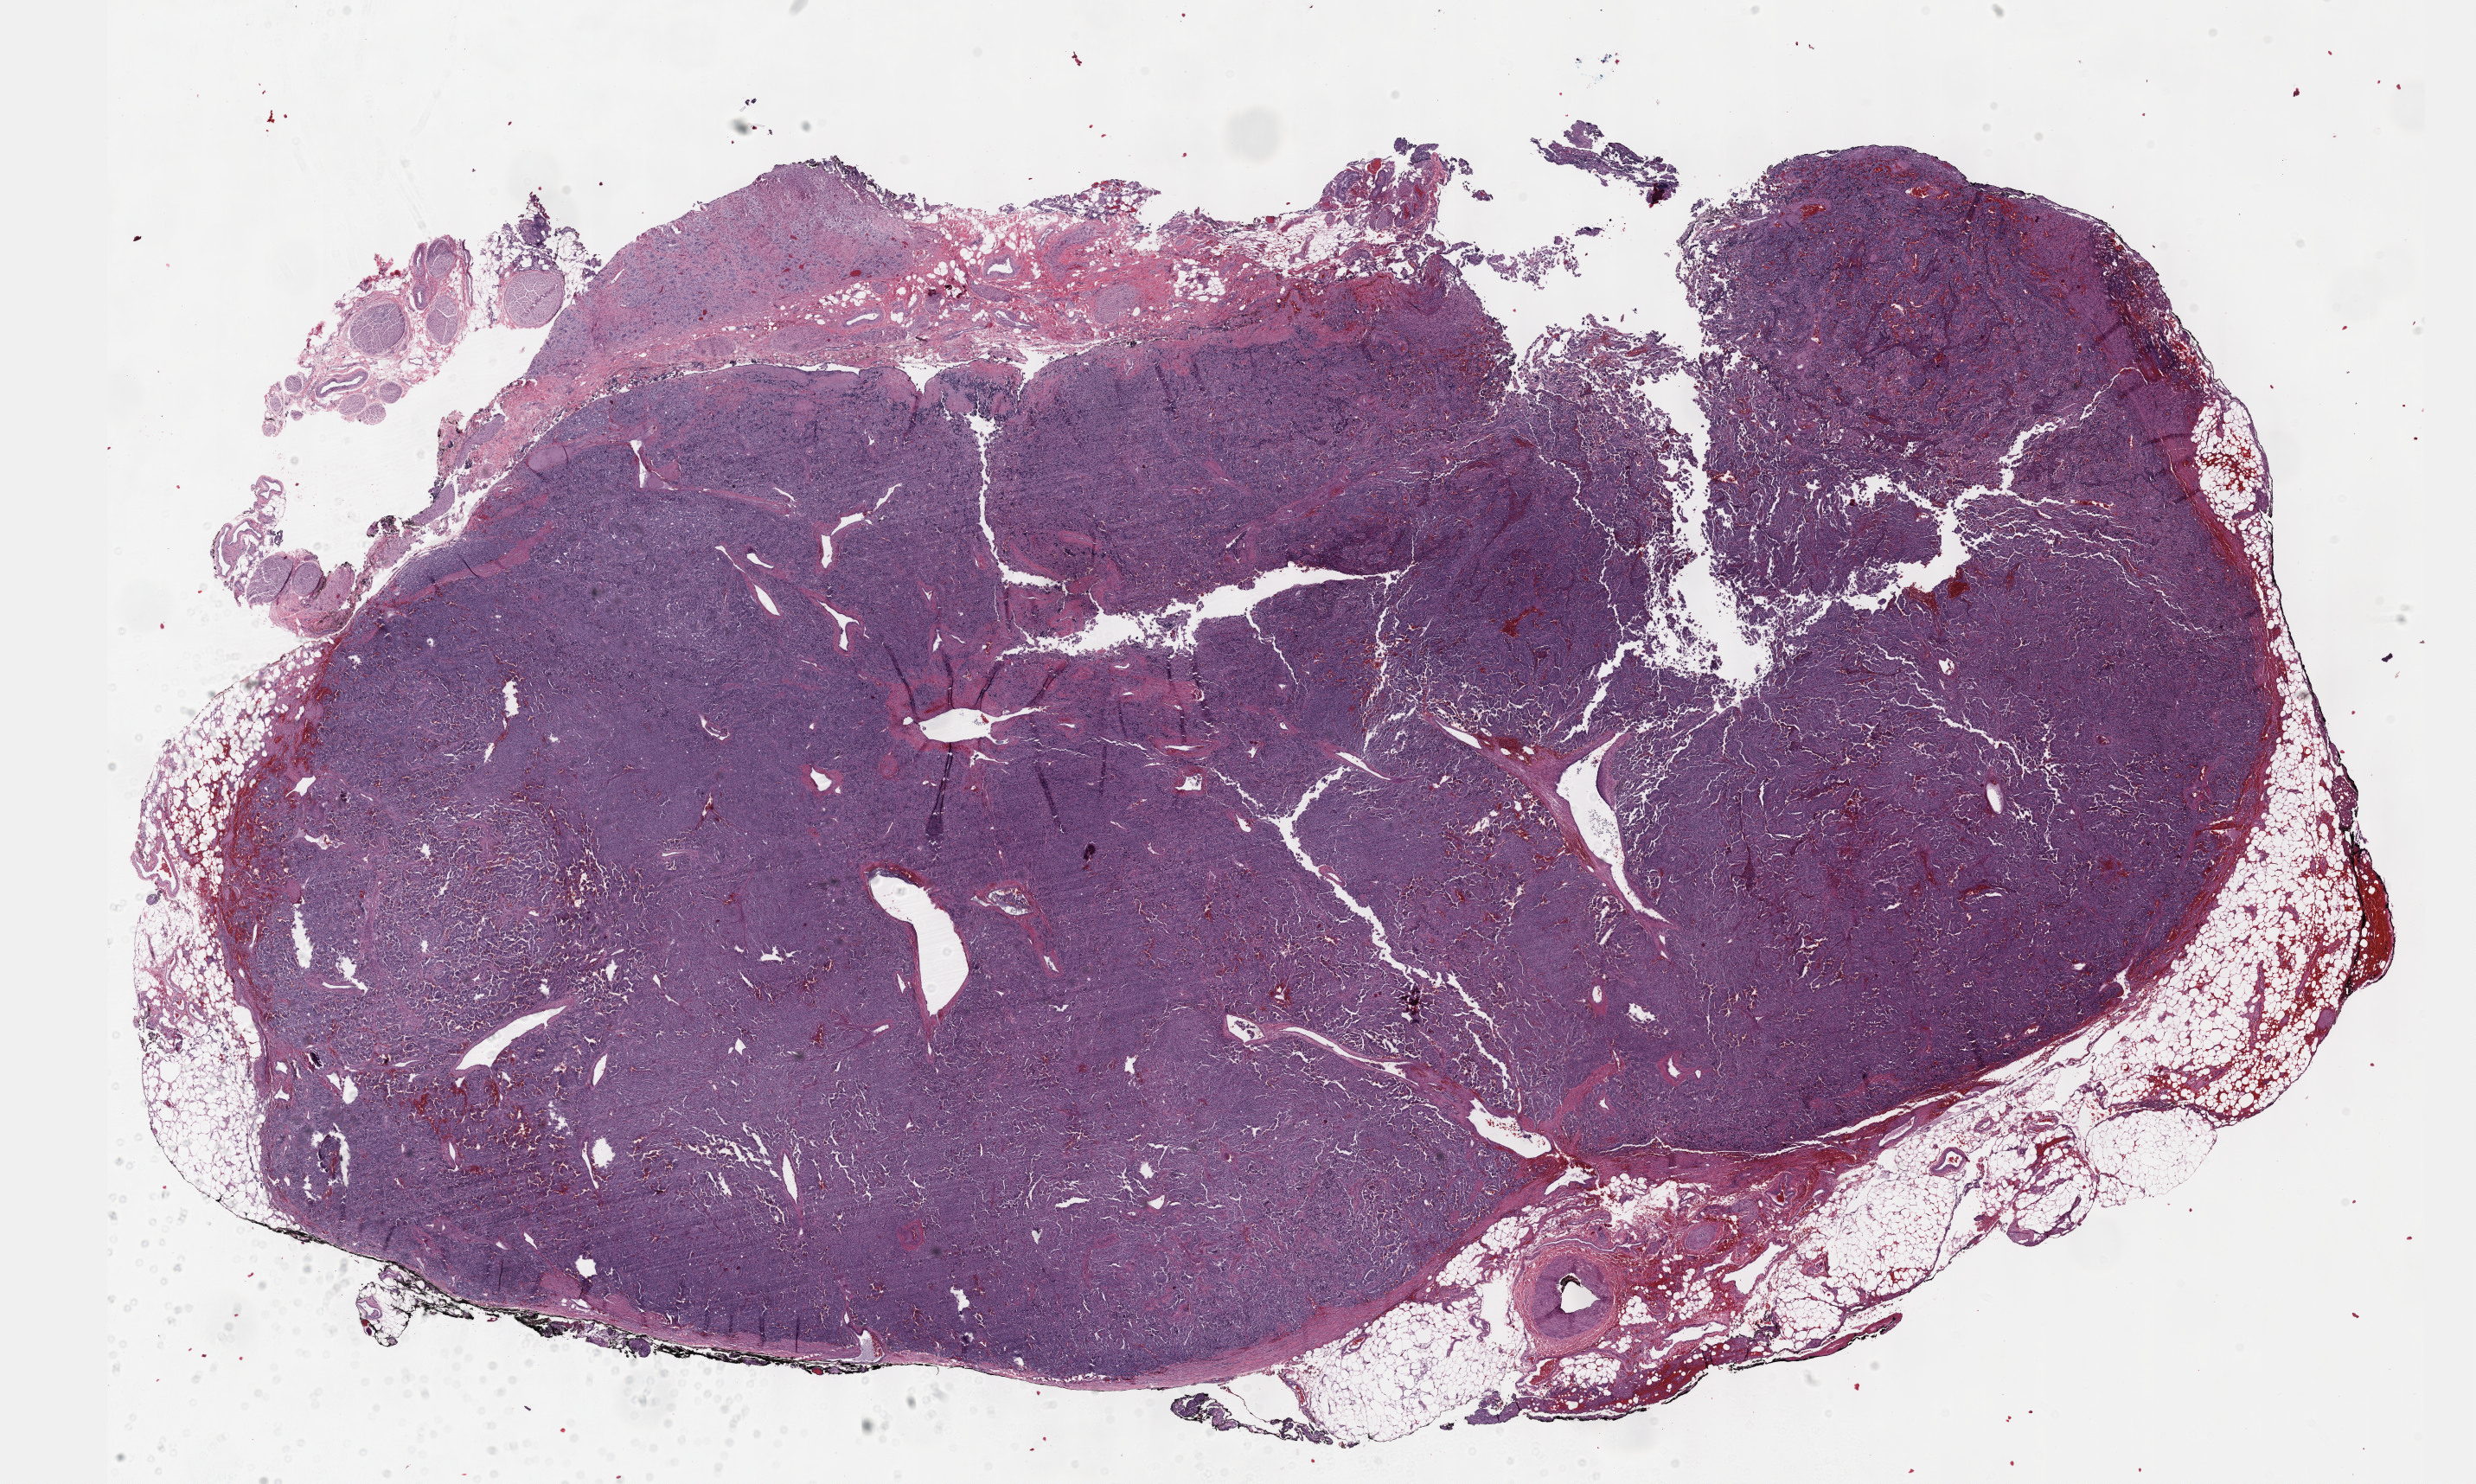
Digitized H&E-stained tissue section (whole slide) — whole scanned area (about 23.1 x 13.9 mm) shown as a low-resolution overview; FFPE section; primary tumour sample from the retroperitoneum and peritoneum. Patient: male, age at initial diagnosis 41 years.
Diagnosis: Extra-adrenal paraganglioma, malignant. Lymph nodes positive (case pathology): 0 of 1 examined.